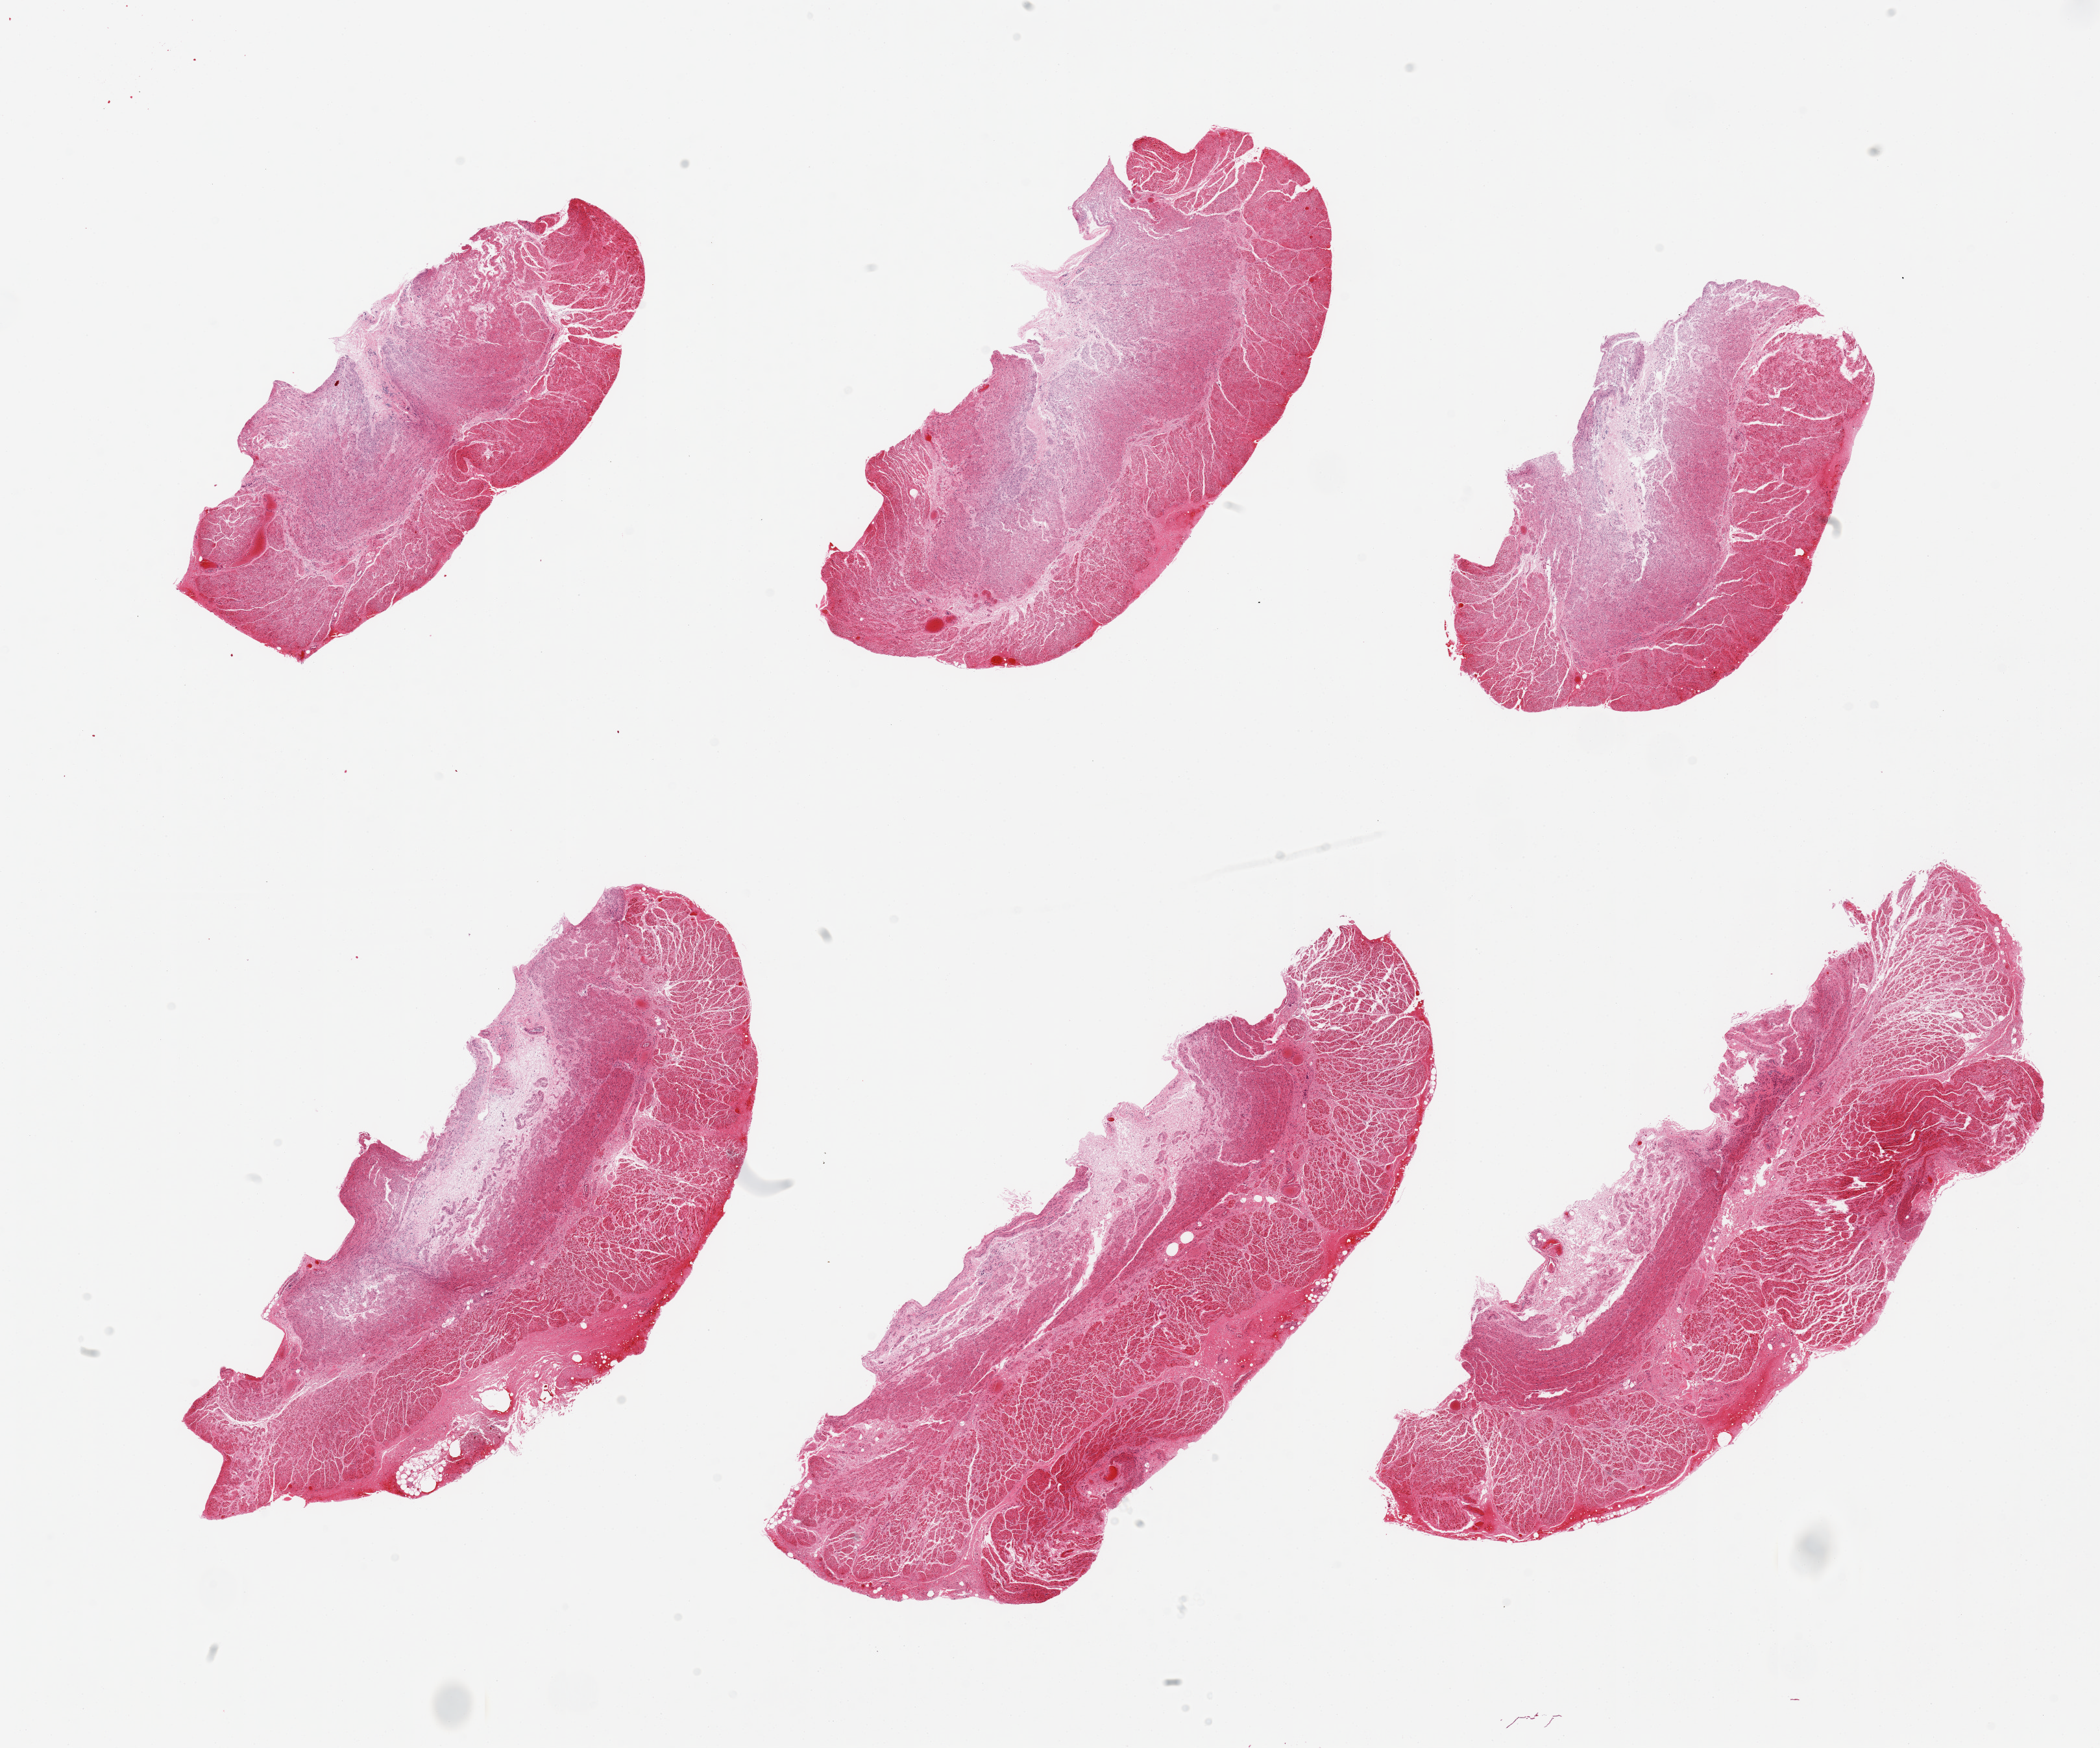
Whole-slide image, H&E stain, a low-resolution overview of the entire scanned area, about 25.6 x 21.3 mm, PAXgene-fixed paraffin-embedded (PFPE) section, sampled site (target tissue): gastroesophageal junction, donor tissue sample. Donor sex: female.
• review note (as recorded): 6 pieces, muscularis, patchy areas of infarction/total autolysis